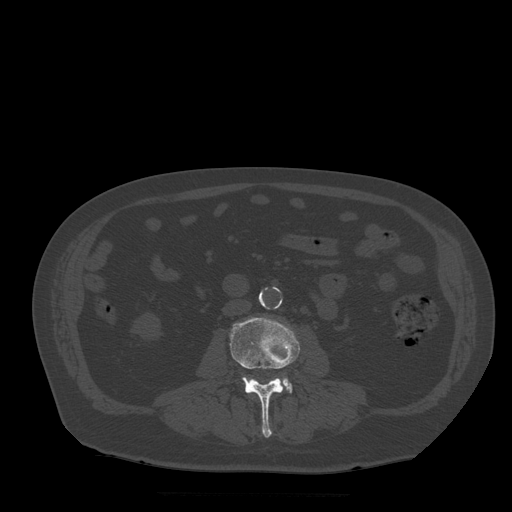
CT including the spine, one axial slice; slice 137 of 522 in the series (ordered by position); bone window (W 1800 / L 400 HU); 1.25 mm slice thickness; 512 × 512 image matrix, field of view 420 × 420 mm. Patient age 72 years. Case-level facts recorded for this patient, not image findings: primary cancer: prostate.
Outlined on this slice (semi-automatic segmentation, software-assisted and operator-edited):
- L3 vertebra: bounding box <230,317,300,438> (left, top, right, bottom; pixels)
- L4 vertebra: <245,377,292,393>